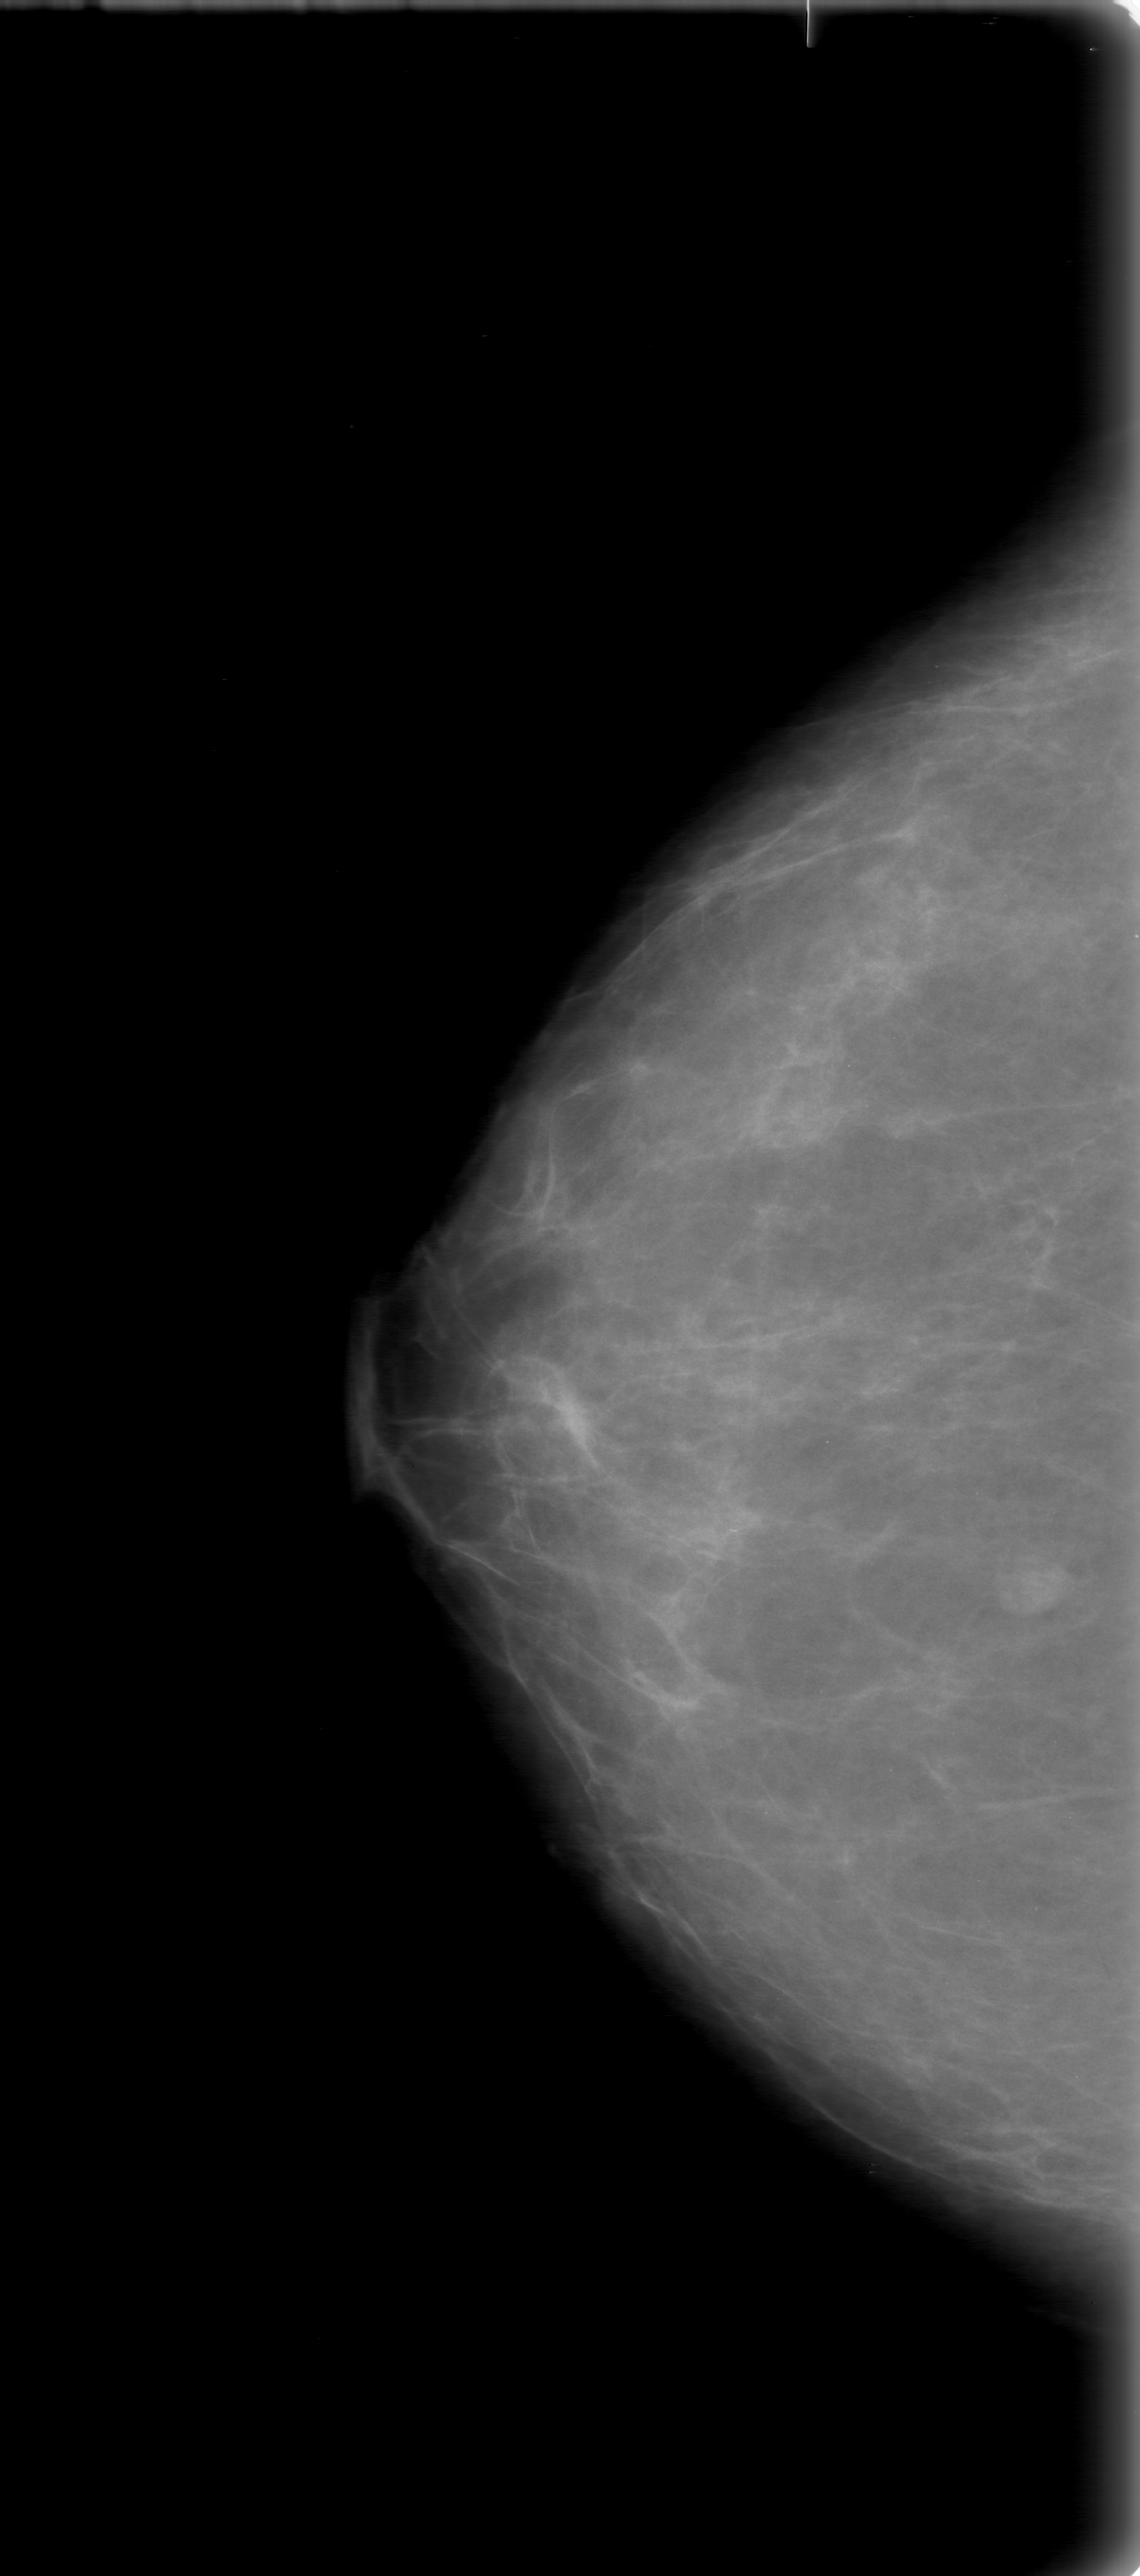
Scanned film-screen mammogram; right breast; CC view; BI-RADS breast density category 1 (scale 1–4).
- Finding: mass, shape lobulated, margins obscured; BI-RADS assessment category 0 (incomplete: needs additional imaging); subtlety rating 4 on a 1 (subtle) to 5 (obvious) scale; pathology result (as recorded, not read from the image): benign.